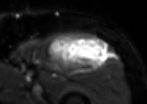
MRI of an extremity soft-tissue mass, one axial slice; T2-weighted fat-saturated; MR volume resampled by the dataset authors to the PET/CT grid (not the native acquisition matrix); 147 × 104 image matrix, field of view 144 × 102 mm. Male patient. From the clinical record (not read from this slice): histological type: extraskeletal osteosarcoma; grade: high; site of the primary tumour: thigh.
Structures marked on this image (expert contour drawn on MRI and transferred to this co-registered scan by the dataset authors):
- gross tumour volume (mass): bounding box [x1, y1, x2, y2] px = [46, 35, 111, 70]